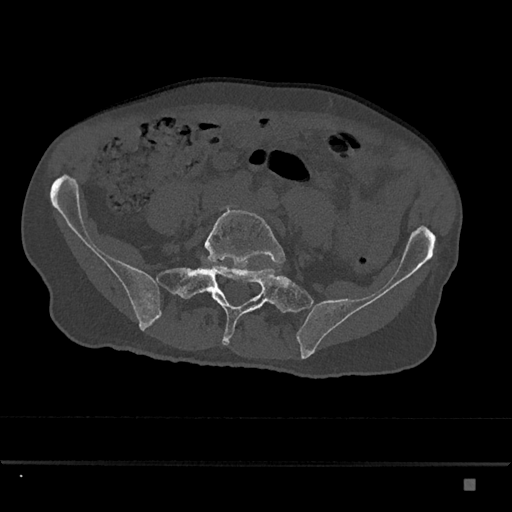
CT including the spine, one axial slice; slice 248 of 797 in the series (ordered by position); 120 kVp; bone window (W 1800 / L 400 HU); 0.5 mm slice thickness; 512 × 512 image matrix, field of view 390 × 390 mm. Male patient, age 72 years. Case-level facts recorded for this patient, not image findings: primary cancer: prostate.
Structures marked on this image (semi-automatic segmentation, software-assisted and operator-edited):
- L5 vertebra: bounding box (x1, y1, x2, y2) in pixels: (204, 205, 286, 266)